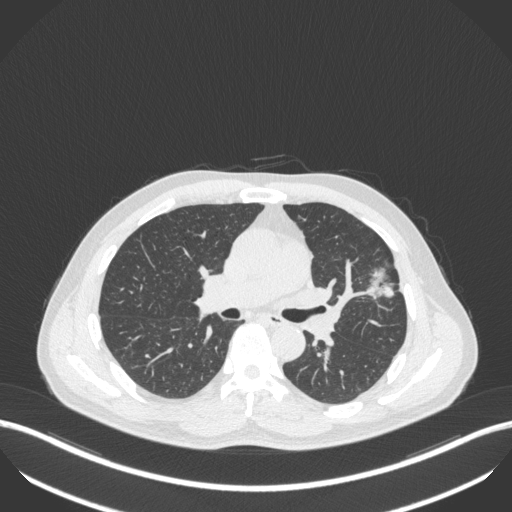
Chest CT, one axial slice; slice 230 of 418 in the series (ordered by position); reconstruction kernel B31f; 120 kVp; lung window (W 1500 / L -600 HU); 1 mm slice thickness; 512 × 512 image matrix, field of view 400 × 400 mm. Patient: male, 55 years. From the clinical record (not read from this slice): clinical TNM (as recorded): T1c N0 M0; histopathological grade: G2-3.
Structures marked on this image (rectangle marked by the reading radiologist):
- lung tumour (recorded histology: adenocarcinoma): bounding box (x1, y1, x2, y2) in pixels: (369, 268, 399, 302)